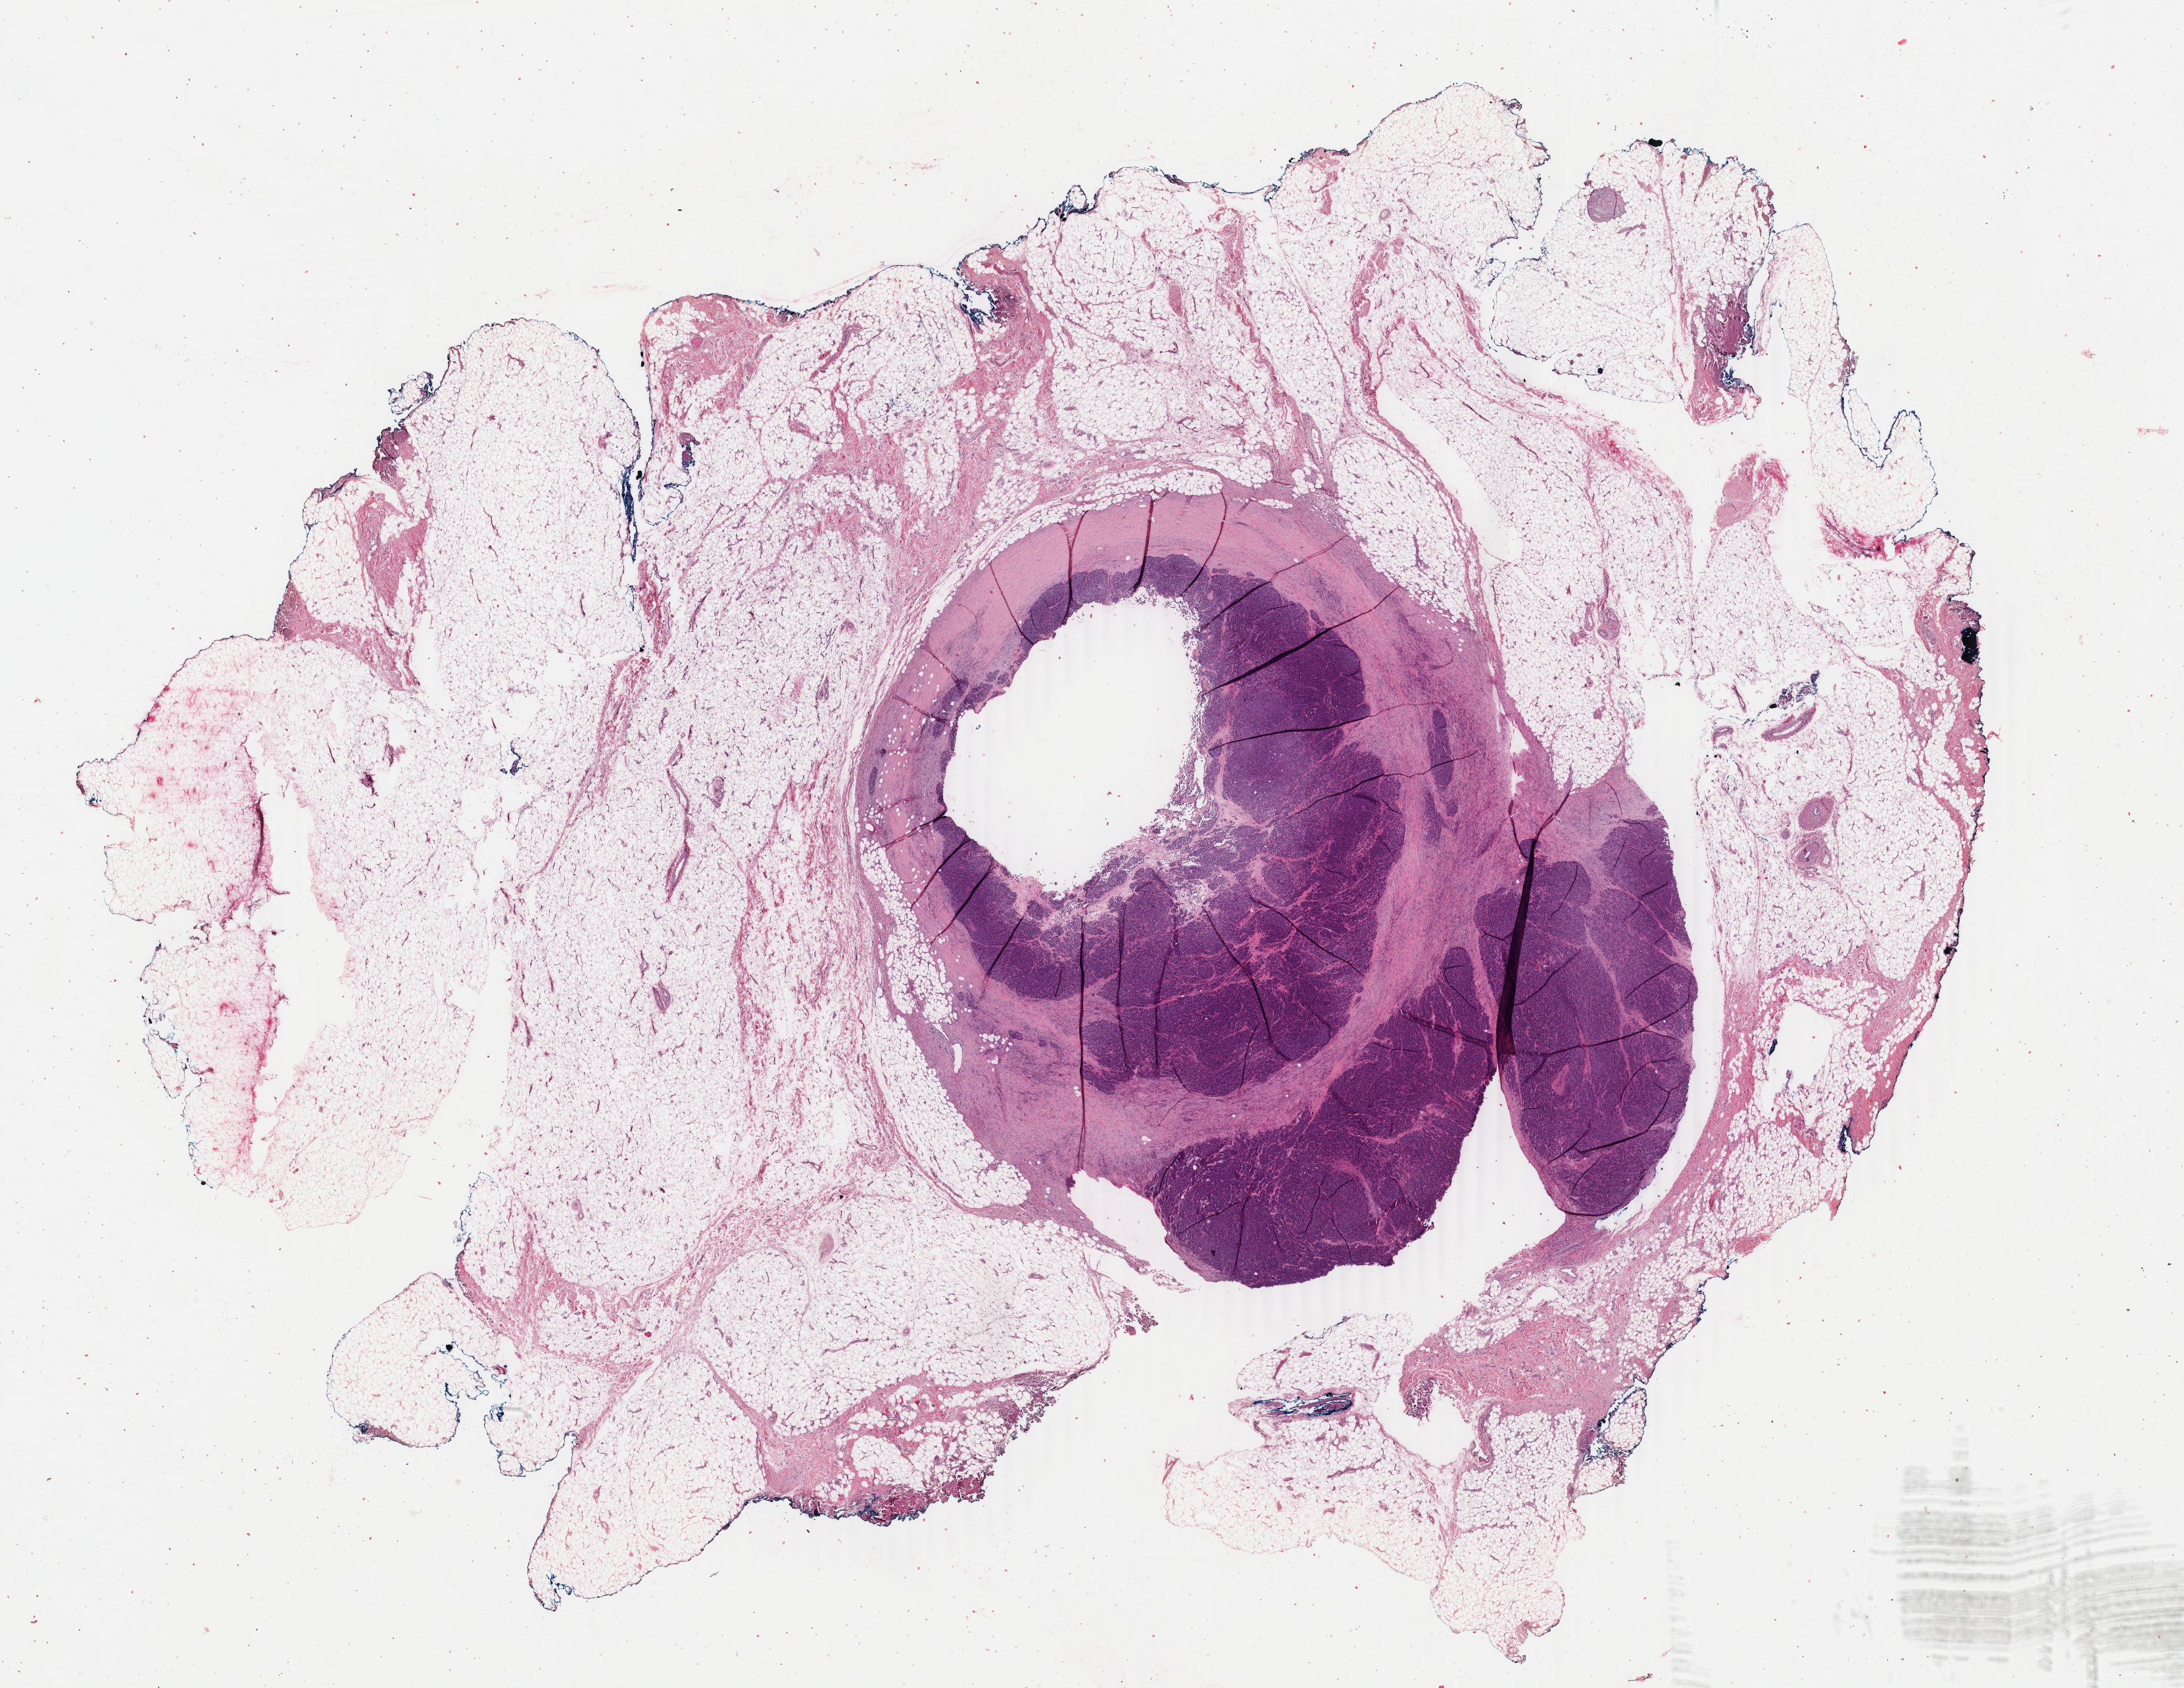
Whole-slide histology image, H&E-stained — low-resolution overview of the scanned area, about 26.4 x 20.4 mm (slide scanned at 40x), formalin-fixed paraffin-embedded (FFPE) diagnostic section, skin, primary tumour sample. Patient: male, age at initial diagnosis 68 years.
Diagnosis: Malignant melanoma, NOS.